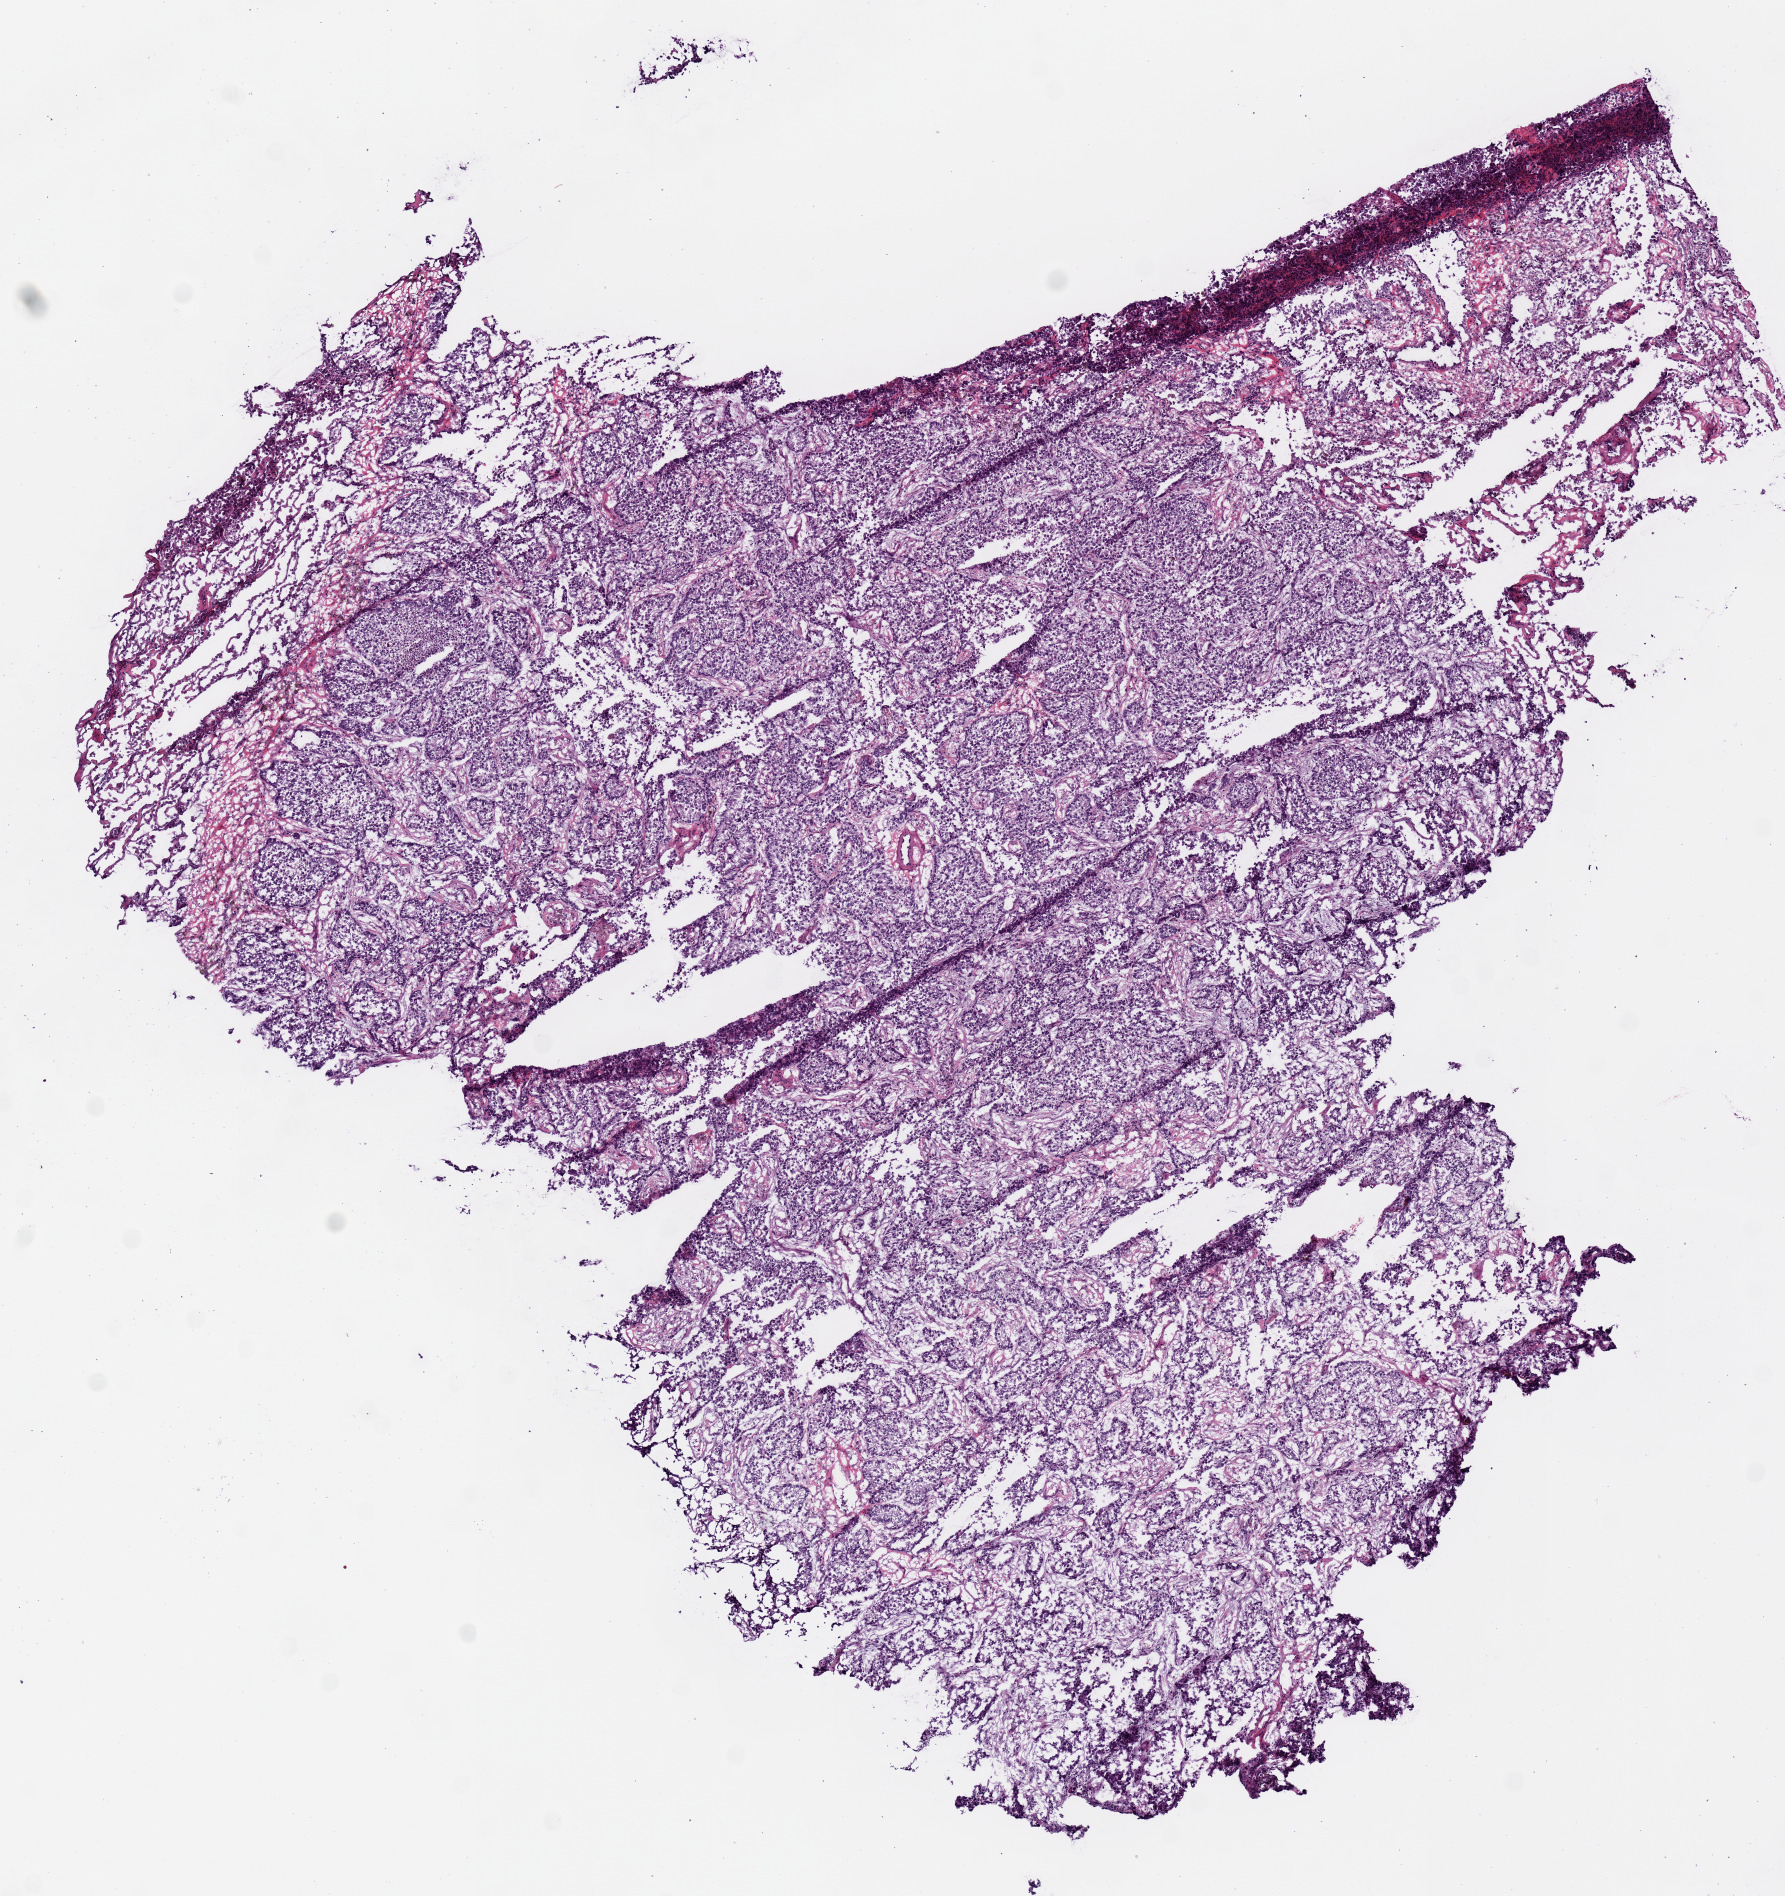
Whole-slide histology image, Hematoxylin and eosin (H&E) stained — a low-resolution overview of the entire scanned area, about 7.1 x 7.5 mm, frozen section from the top of the tissue portion, primary tumour sample from the lung. Male, age 53 years at initial diagnosis. Slide review estimates, as recorded: tumour cells 82%, tumour nuclei 80%, normal cells 8%, stromal cells 10%, necrosis 0%.
* AJCC pathologic stage: IA (7th edition)
* diagnosis: Adenocarcinoma, NOS (upper lobe, lung)